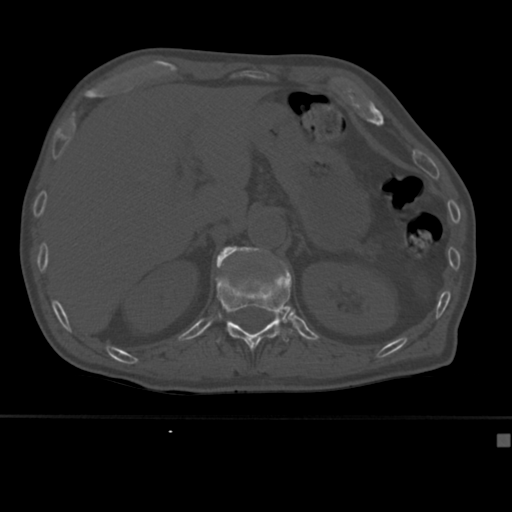
CT including the spine, one axial slice; slice 188 of 430 in the series (ordered by position); 120 kVp; bone window (W 1800 / L 400 HU); 512 × 512 image matrix. Male patient, age 64 years. Case-level facts recorded for this patient, not image findings: primary cancer: uterus; vertebrae with lytic lesions (as recorded): T1, T4, T5, T7, L5.
Outlined on this slice (semi-automatic segmentation, software-assisted and operator-edited):
- L1 vertebra: bounding box (x1, y1, x2, y2) in pixels: (216, 246, 270, 267)
- T12 vertebra: (216, 268, 292, 351)